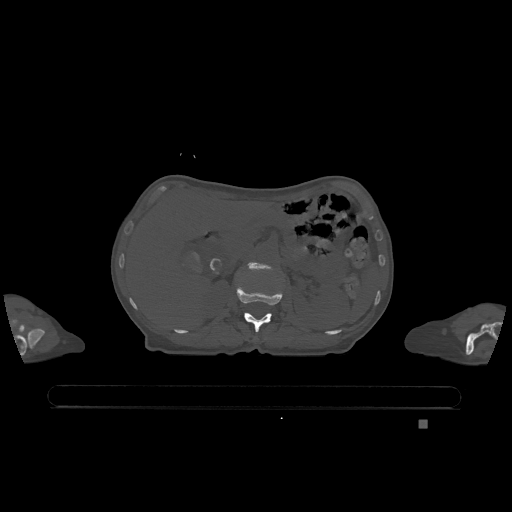
CT including the spine, one axial slice. Slice 466 of 1317 in the series (ordered by position). Bone window (W 1800 / L 400 HU). 512 × 512 image matrix. Female patient, age 74 years. Case-level facts recorded for this patient, not image findings: primary cancer: lung; vertebrae with lytic lesions (as recorded): T1, T4, T5, T6, L4, L5.
Annotated regions visible in this slice (semi-automatically segmented with operator editing):
- L1 vertebra: box from (x=237, y=284) to (x=283, y=332) px
- L2 vertebra: (x=249, y=263)–(x=270, y=271)